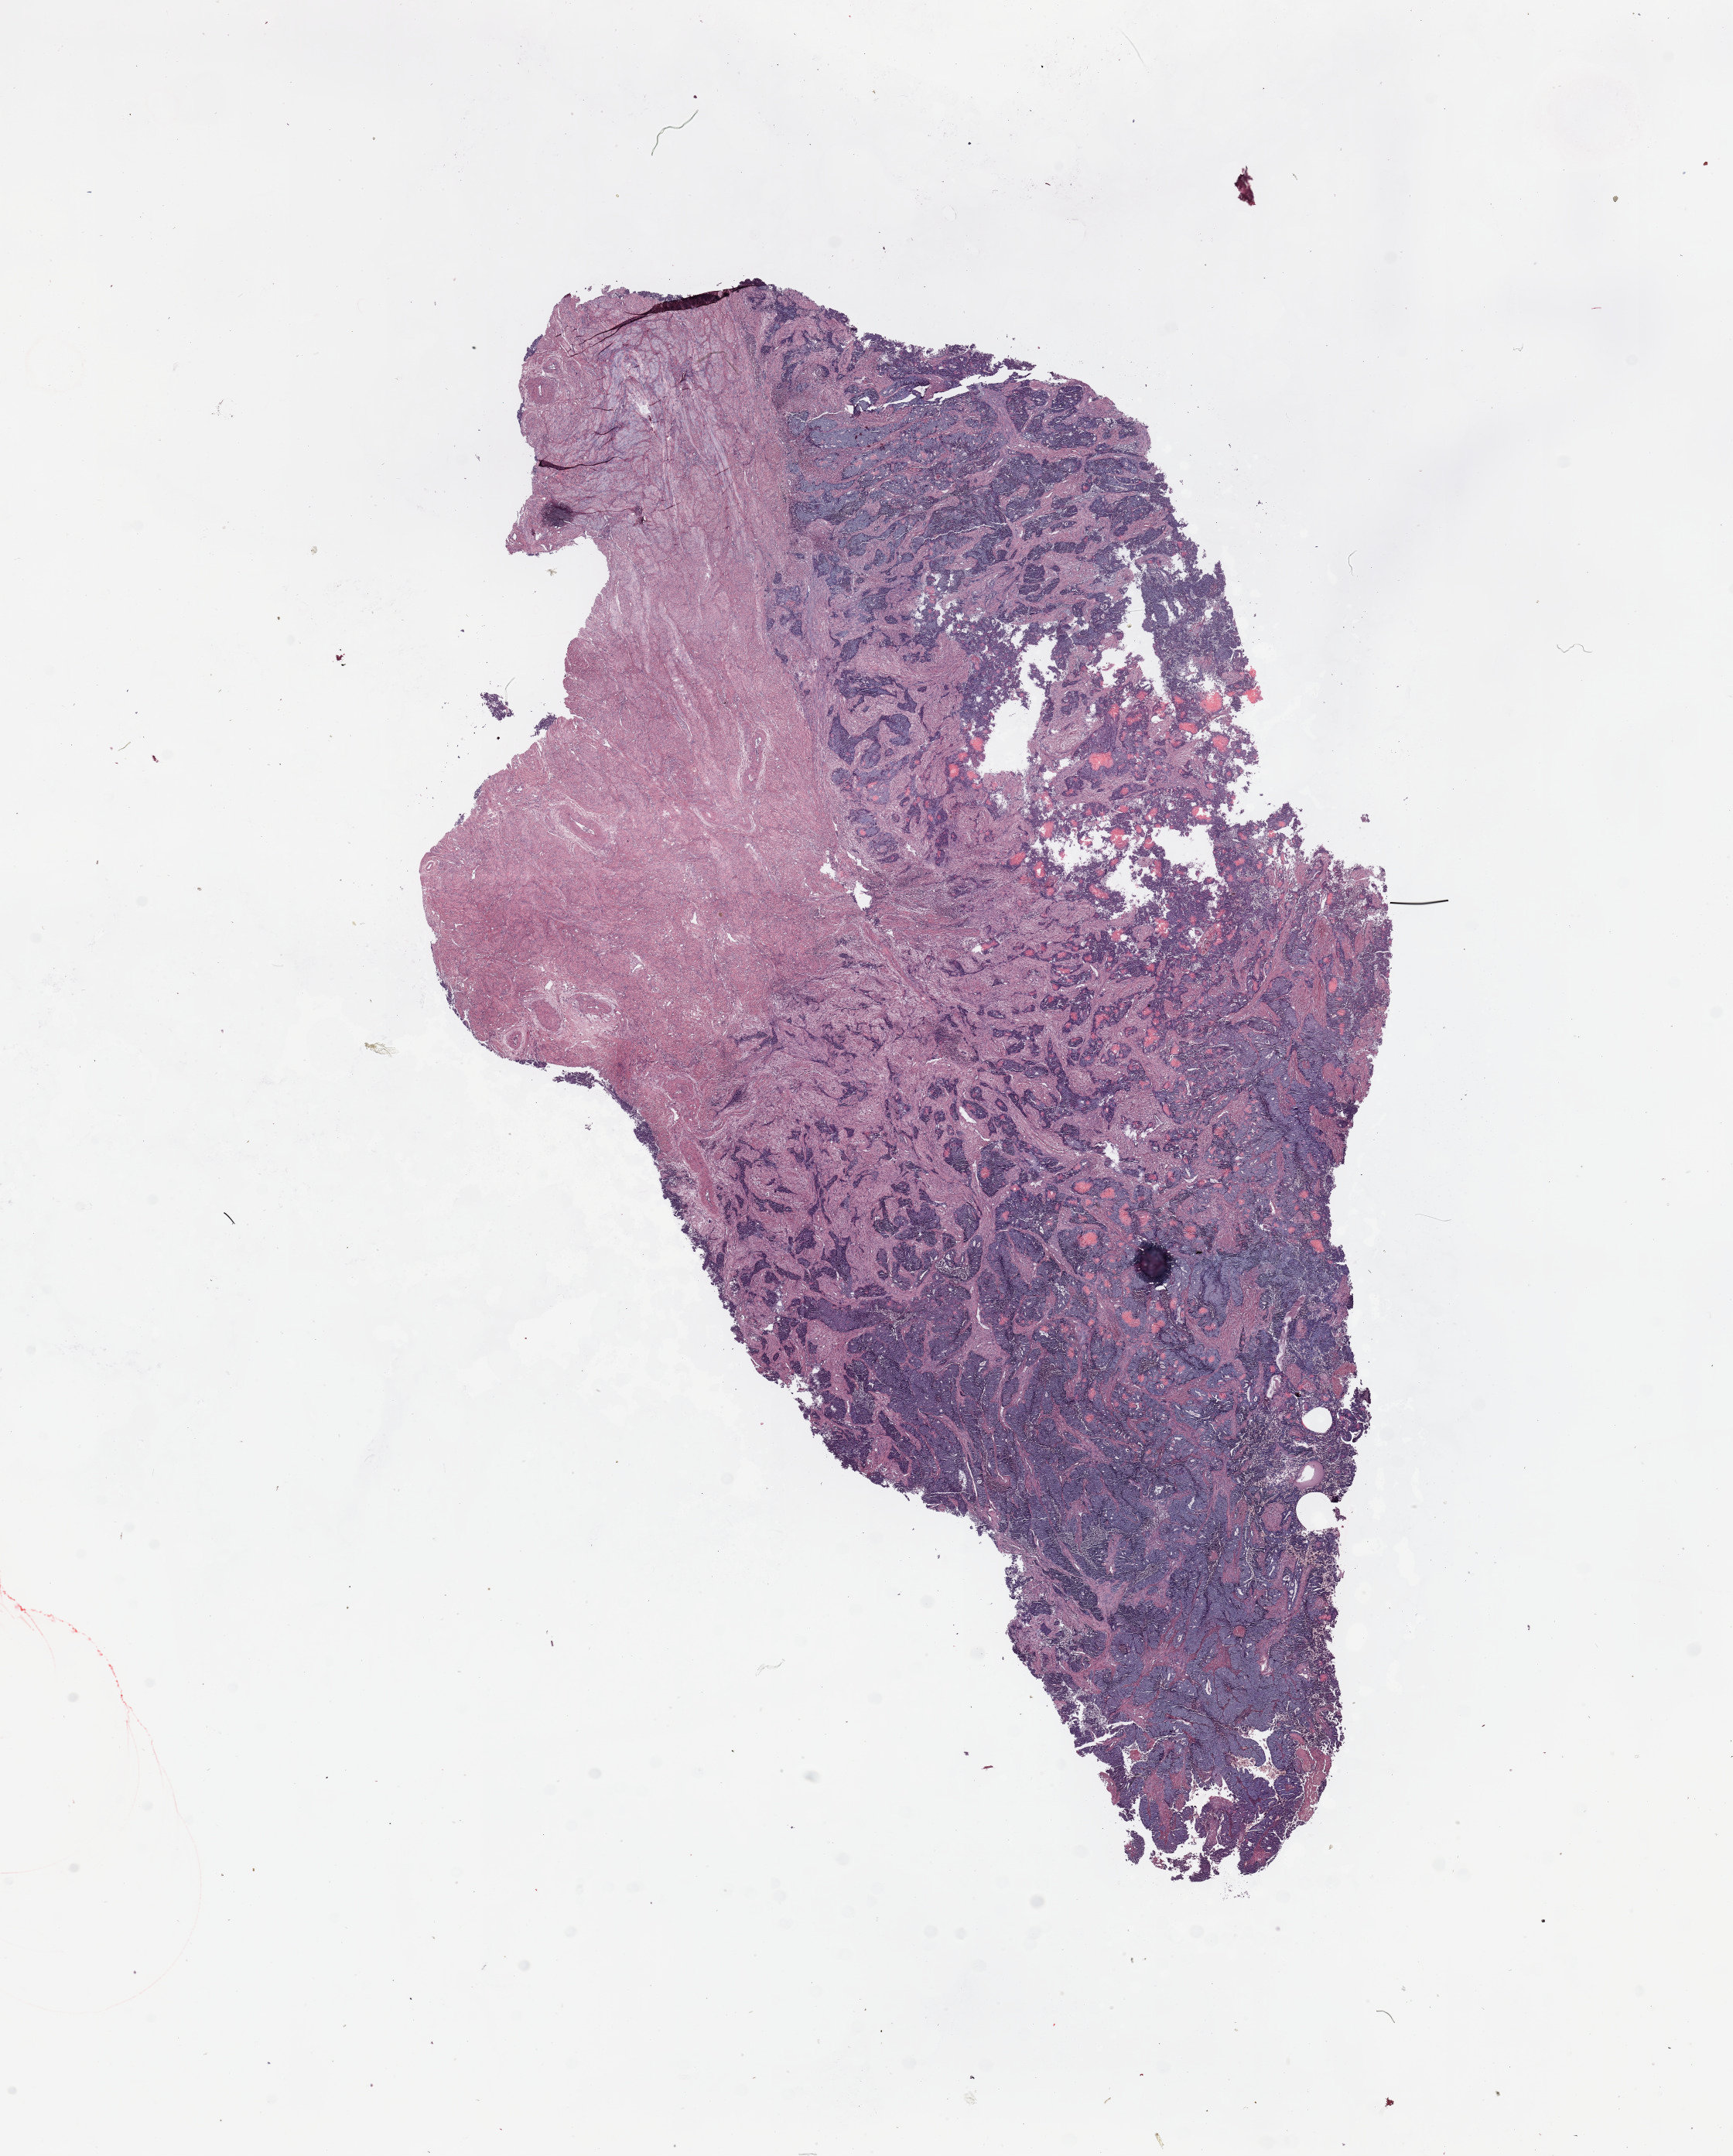
Whole-slide histology image, H&E — whole scanned area (about 17.7 x 22.0 mm, from a 20x scan) shown as a low-resolution overview, uterus, tumour tissue. Female, 59 y/o. Histologic grade: G2 (moderately differentiated).
• diagnosis: Endometrioid adenocarcinoma, NOS
• AJCC pathologic stage: II